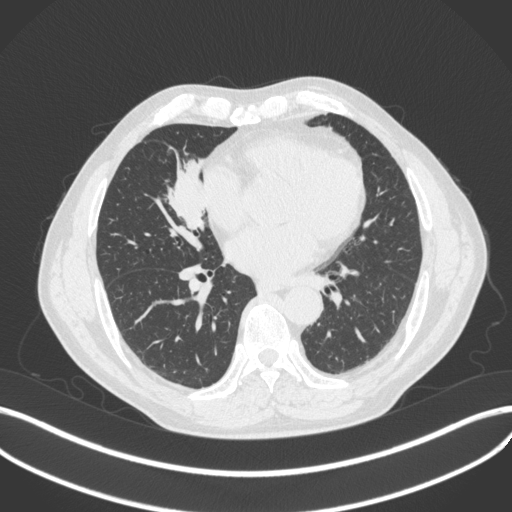
Chest CT, one axial slice; slice 175 of 429 in the series (ordered by position); reconstruction kernel B31f; lung window (W 1500 / L -600 HU); 1 mm slice thickness; 512 × 512 image matrix, field of view 400 × 400 mm. Male patient, age 61 years. From the clinical record (not read from this slice): clinical TNM (as recorded): T2b N1 M0.
Annotated regions visible in this slice (rectangle marked by the reading radiologist):
- lung tumour (recorded histology: squamous cell carcinoma): box from (x=163, y=150) to (x=211, y=233) px